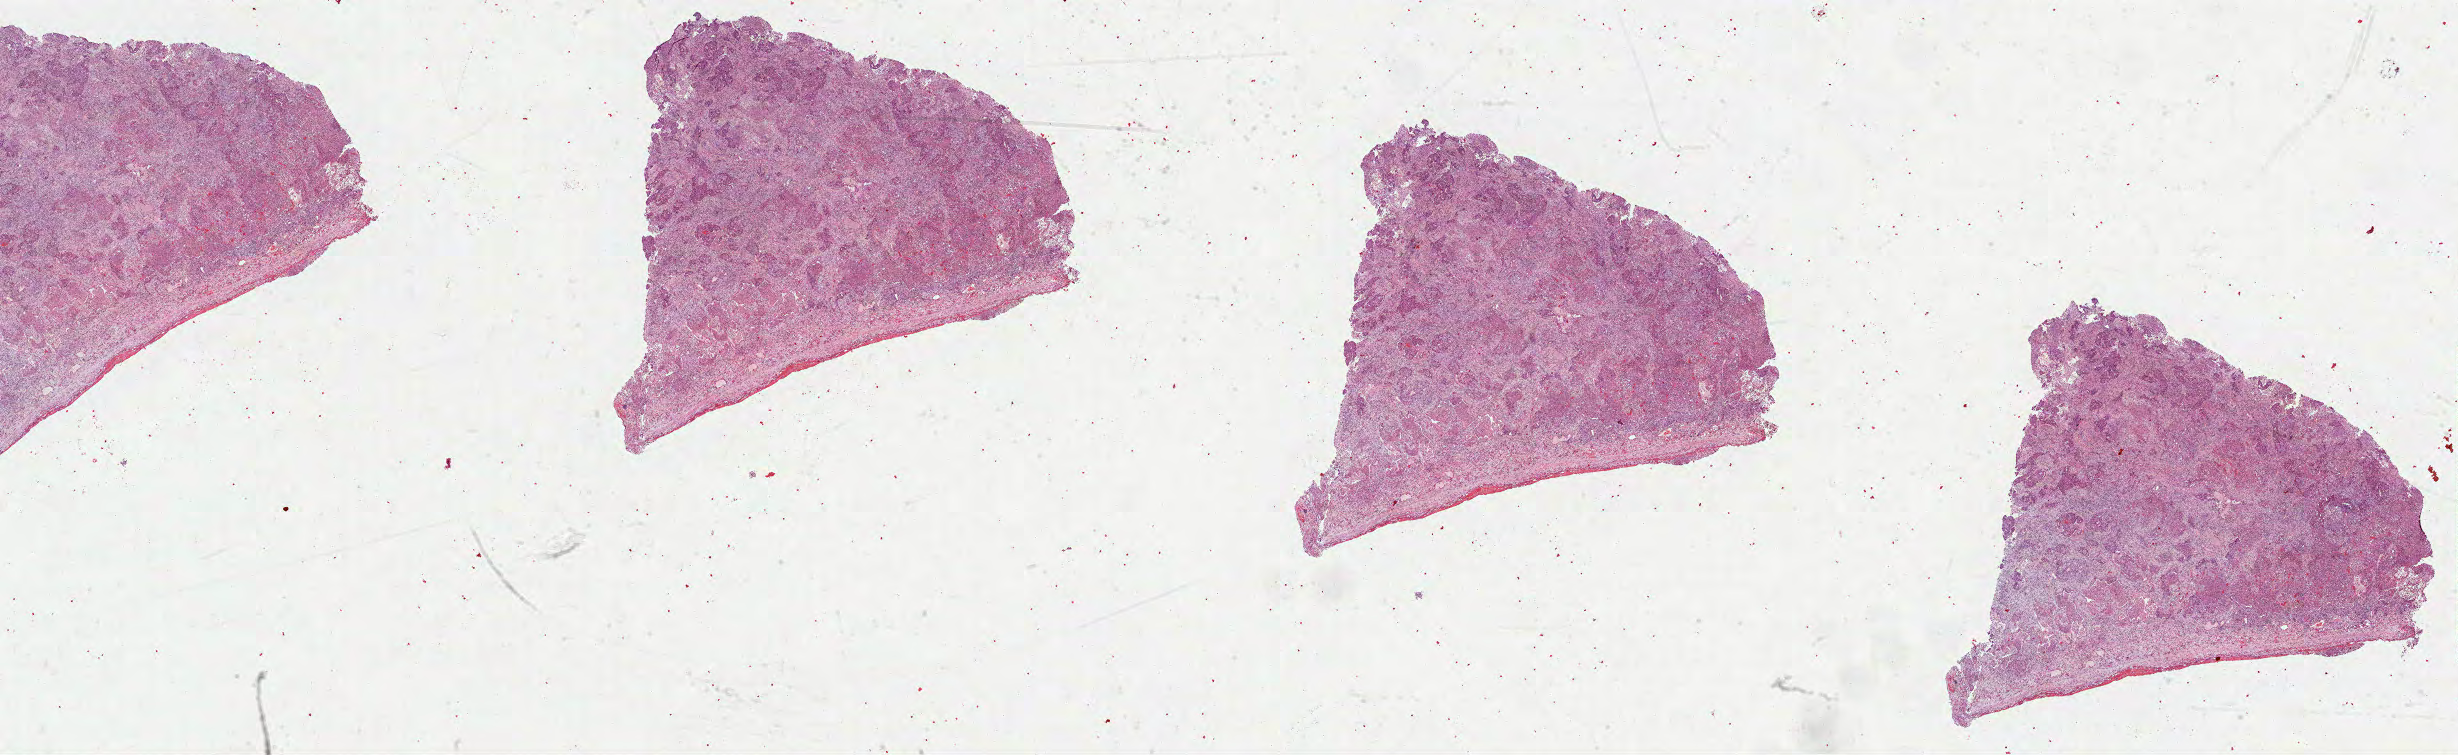
Digitized H&E-stained tissue section (whole slide), whole scanned area (about 39.6 x 12.2 mm) shown as a low-resolution overview, formalin-fixed paraffin-embedded (FFPE) diagnostic section, primary tumour sample from the lung. Male patient; age at initial diagnosis 65 years.
• AJCC pathologic stage: IB (6th edition)
• diagnosis: Adenocarcinoma, NOS (upper lobe, lung)
• laterality: right